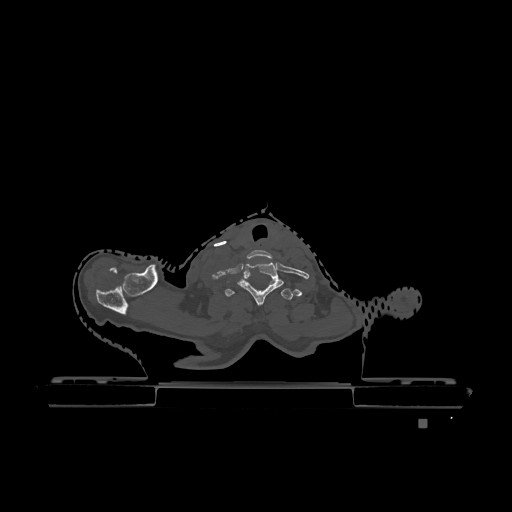
CT including the spine, one axial slice. Position 1023 of 1317 along the scan axis. Bone window (W 1800 / L 400 HU). 512 × 512 image matrix, field of view 500 × 500 mm. Female patient, age 74 years. From the clinical record (not read from this slice): primary cancer: lung.
Annotated regions visible in this slice (semi-automatically segmented with operator editing):
- T1 vertebra: box from (x=225, y=281) to (x=293, y=300) px